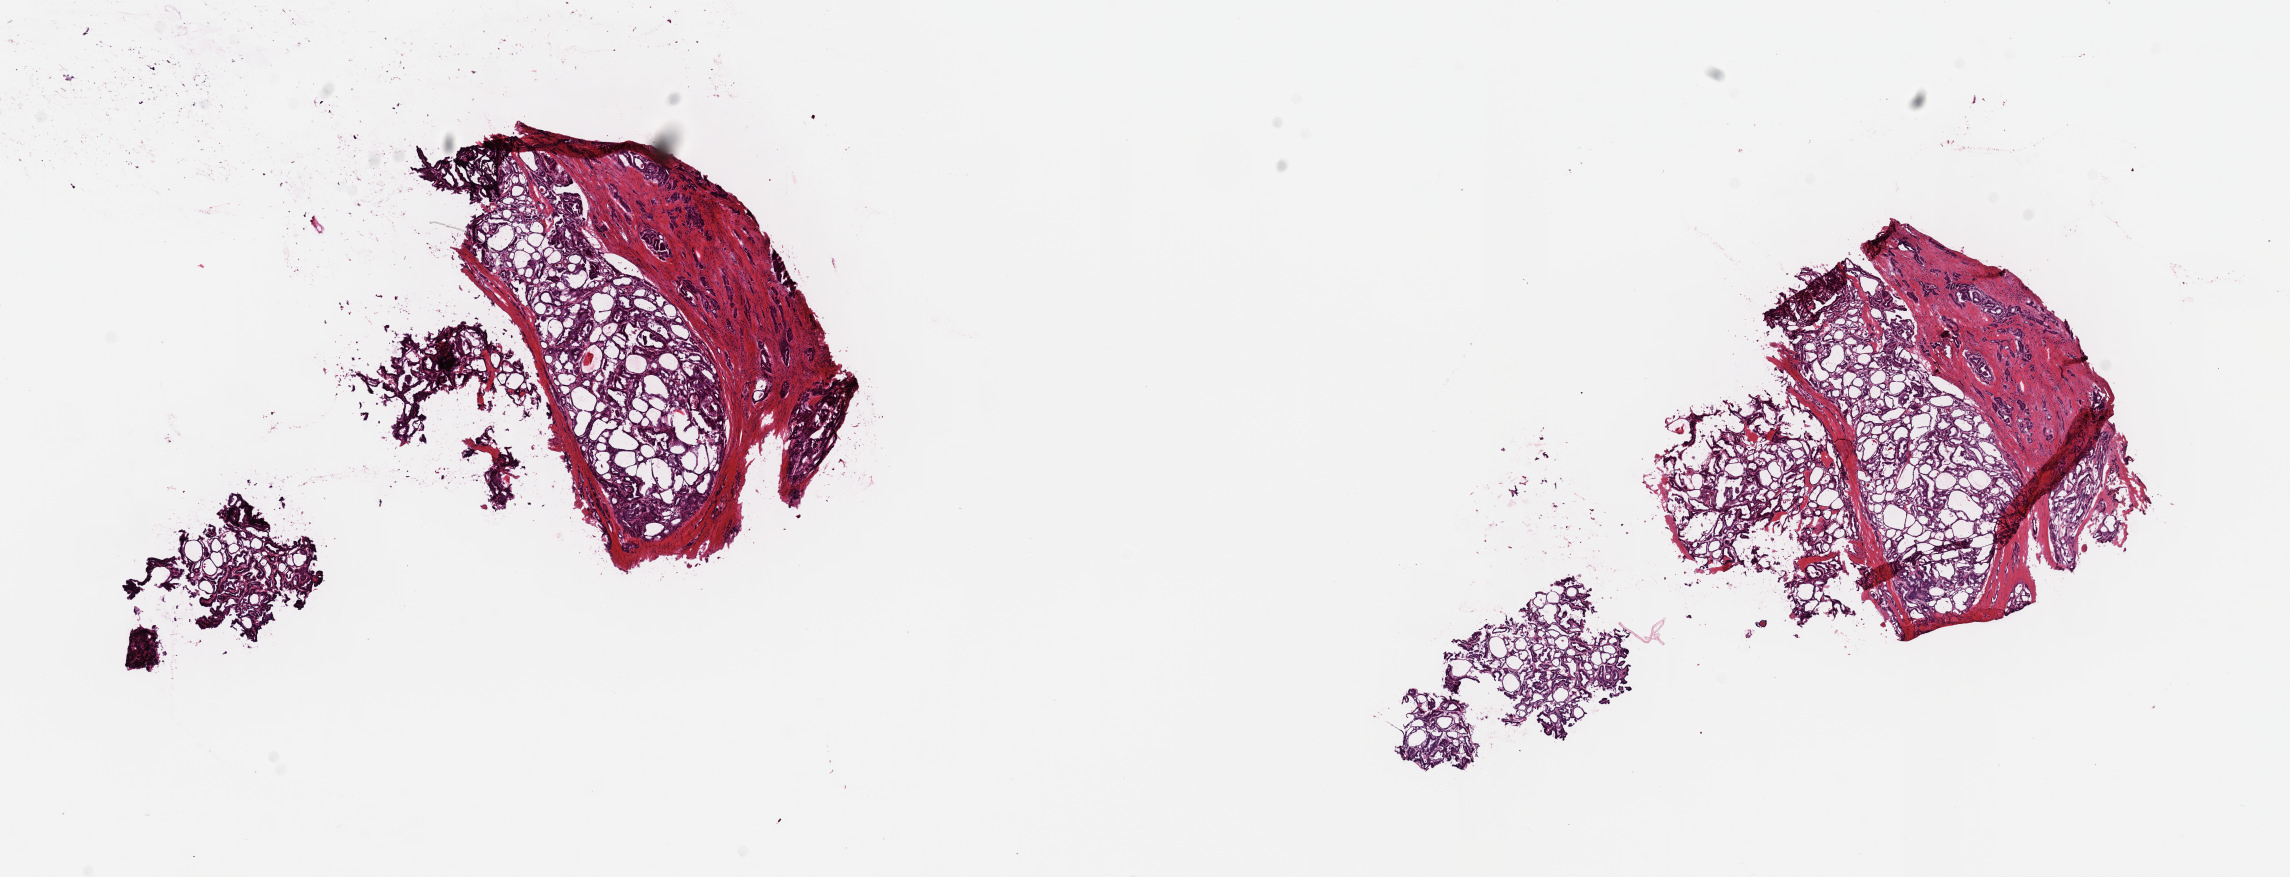
H&E-stained whole-slide image, shown as a low-resolution overview of the whole scanned area (about 18.1 x 6.9 mm, acquisition: 40x scan), frozen section from the top of the tissue portion, sample: primary tumour, thyroid. Female patient; age at initial diagnosis 36 years. Composition of this section per pathologist review: tumour cells 60%, tumour nuclei 95%, normal cells 0%, stromal cells 40%, necrosis 0%. Inflammatory infiltration, as recorded: lymphocyte infiltration 0%, monocyte infiltration 1%, neutrophil infiltration 0%.
* AJCC pathologic stage: I (7th edition)
* lymph nodes positive (case pathology): 27 of 80 examined
* histologic diagnosis: Papillary adenocarcinoma, NOS (thyroid gland)
* laterality: right